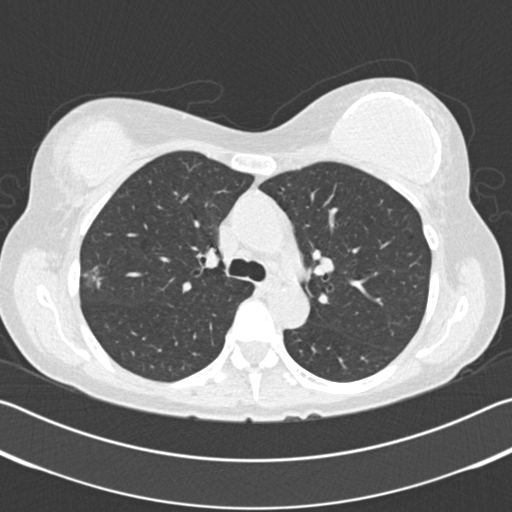
Low-dose screening chest CT, axial slice; second screening round (one year after baseline); lung window (W 1500 / L -600 HU); 120 kVp; slice 59 of 183 in the series; 512 × 512 image matrix, field of view 340 × 340 mm. Female, age 58 years at enrolment. Former smoker at enrolment.
• Expert reader's lesion annotation, bounding box [x1, y1, x2, y2] px = [67, 256, 119, 307].
• Screening reader's record for this exam (one nodule recorded; not confirmed to be the boxed lesion): non-calcified nodule or mass ≥4 mm, right upper lobe, 15 × 13 mm, poorly defined margins, ground glass attenuation, pre-existing on the prior screen: no.
• Participant outcome: lung cancer diagnosed 120 days after this screen — bronchiolo-alveolar adenocarcinoma, NOS, right upper lobe, well differentiated (G1), stage IA (AJCC 6th edition).